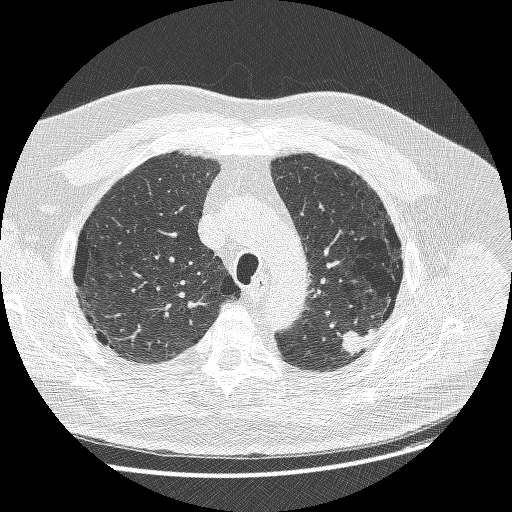
Low-dose screening chest CT, axial slice, baseline annual screen, lung window (W 1500 / L -600 HU), 1.25 mm slice thickness. Male, age 68 years at enrolment. Former smoker at enrolment.
• Expert-annotated lung lesion, bounding box [x1, y1, x2, y2] px = [332, 316, 389, 363].
• The exam's reader record, not a measurement of the box and not confirmed to be the same lesion: non-calcified nodule or mass ≥4 mm, left upper lobe, 15 × 14 mm, smooth margins, soft tissue attenuation.
• Official screen result: positive, change unspecified: nodule(s) >= 4 mm or enlarging nodule(s), mass(es), or other non-specific abnormalities suspicious for lung cancer.
• Participant outcome: lung cancer diagnosed 19 days after this screen — adenosquamous carcinoma, left upper lobe, poorly differentiated (G3), stage IIIB (AJCC 6th edition), 32 mm at pathology.